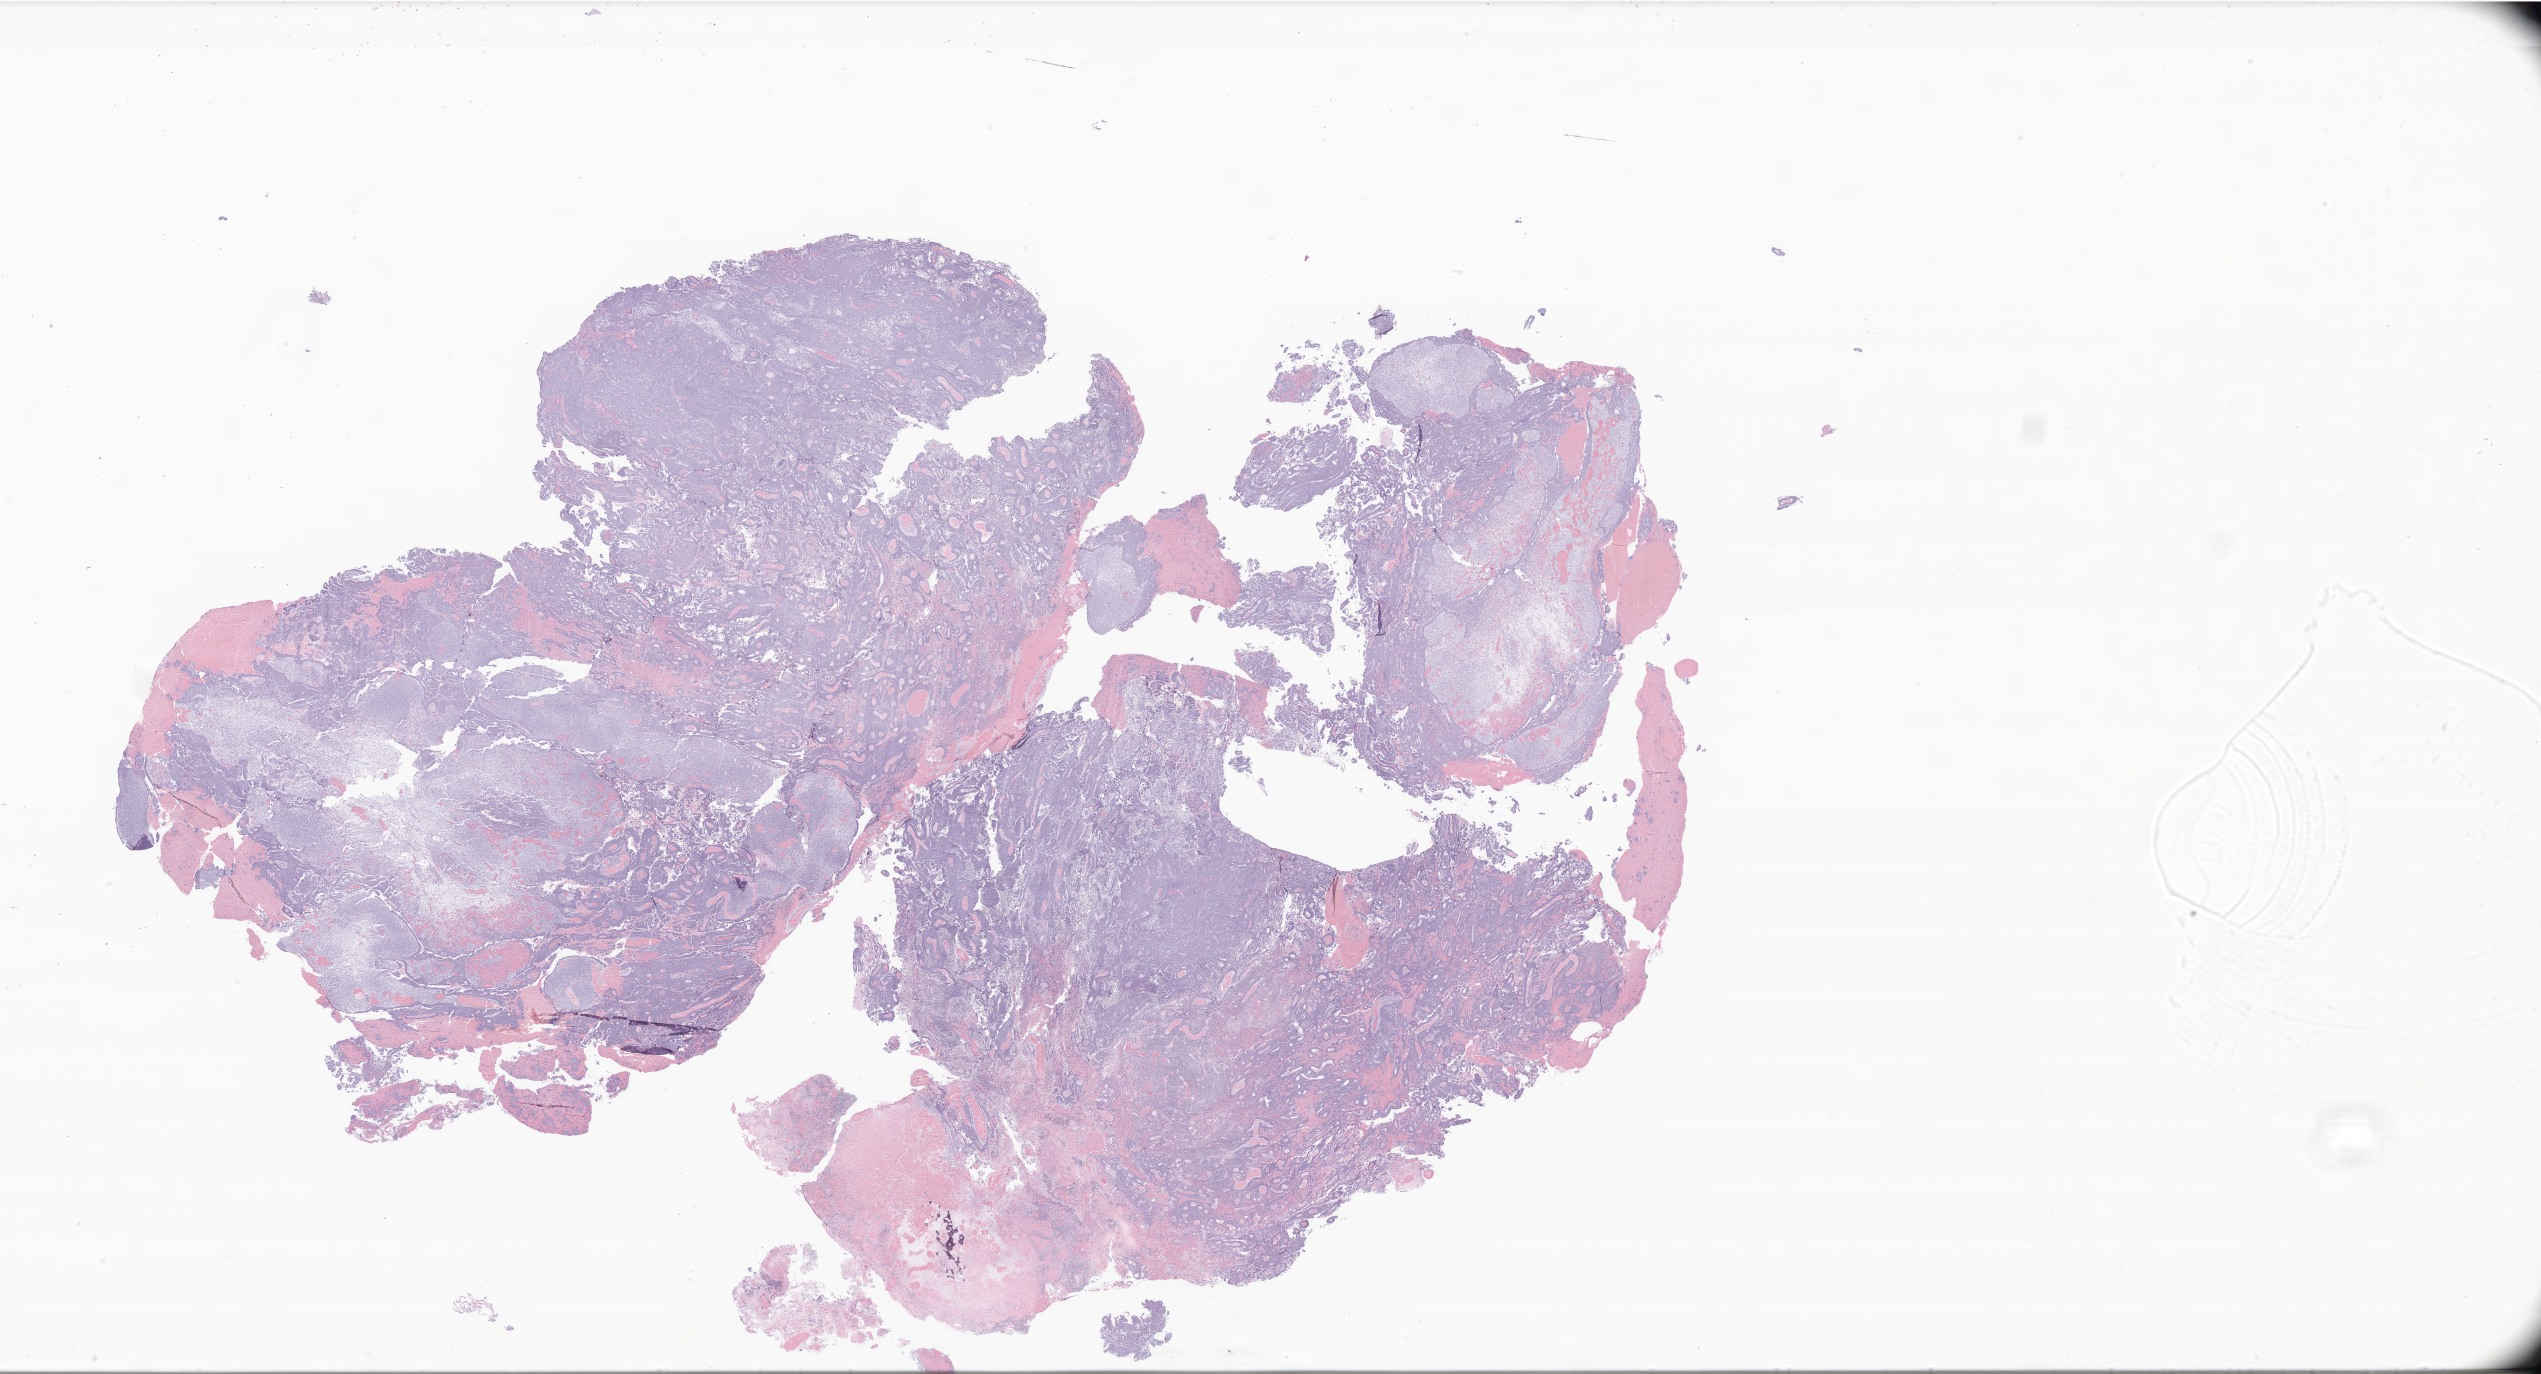
Whole-slide image, haematoxylin and eosin stain of tumor tissue from the brain — shown as a low-resolution overview of the whole scanned area (about 42.9 x 23.2 mm), FFPE section. Female patient, age 40 months.
Diagnosis (ICD-O-3 morphology term): Glioma, malignant.